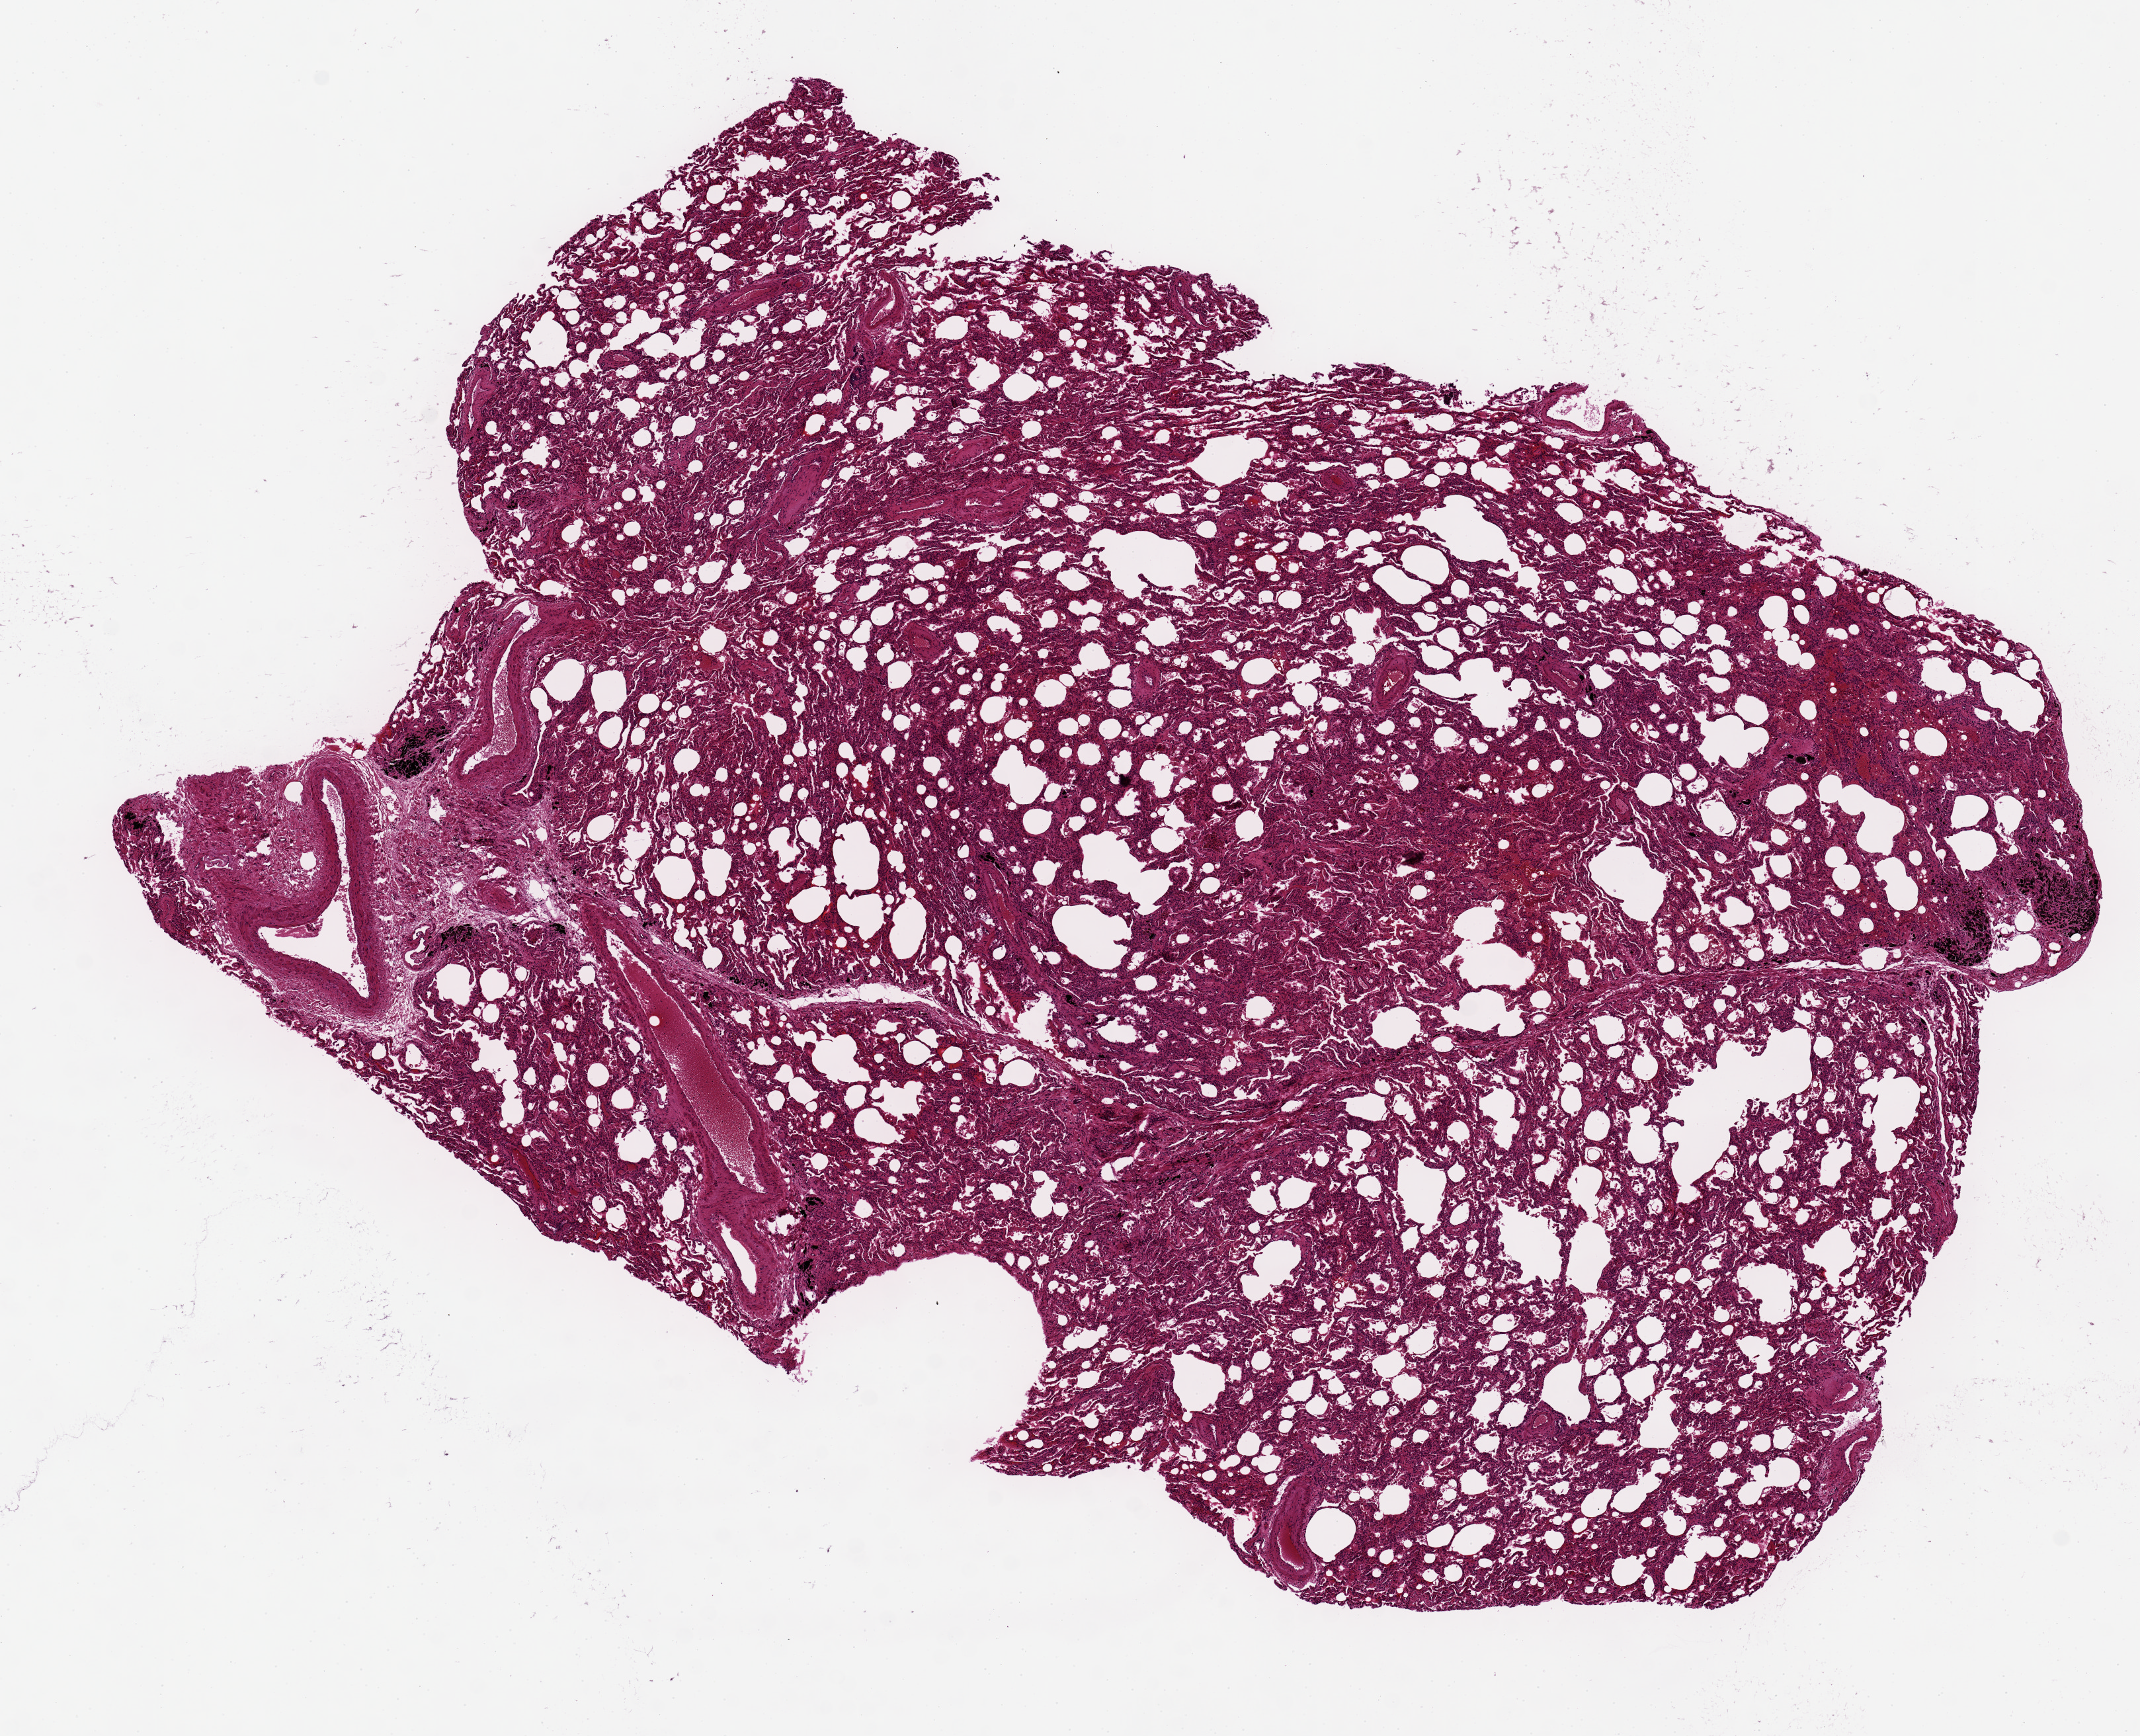
Digitized haematoxylin and eosin-stained section — shown as a low-resolution overview of the whole scanned area (about 12.8 x 10.4 mm); PAXgene-fixed, paraffin-embedded tissue; section of lung (target tissue); donor tissue sample. Donor: male.
- review note (as recorded): mild congestion with atalectasis